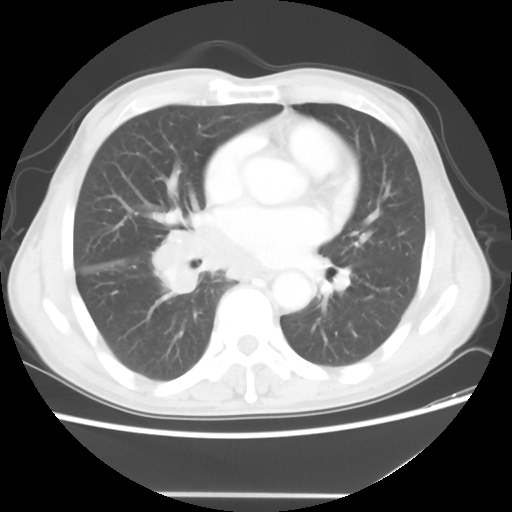
Chest CT, one axial slice. Lung window (W 1500 / L -600 HU). 5 mm slice thickness. 512 × 512 image matrix. Patient: male, 65 years. Case-level facts recorded for this patient, not image findings: clinical TNM (as recorded): T1c N3 M0.
Annotated regions visible in this slice (bounding box drawn by a radiologist):
- lung tumour (recorded histology: small cell carcinoma): bounding box <149,218,272,295> (left, top, right, bottom; pixels)